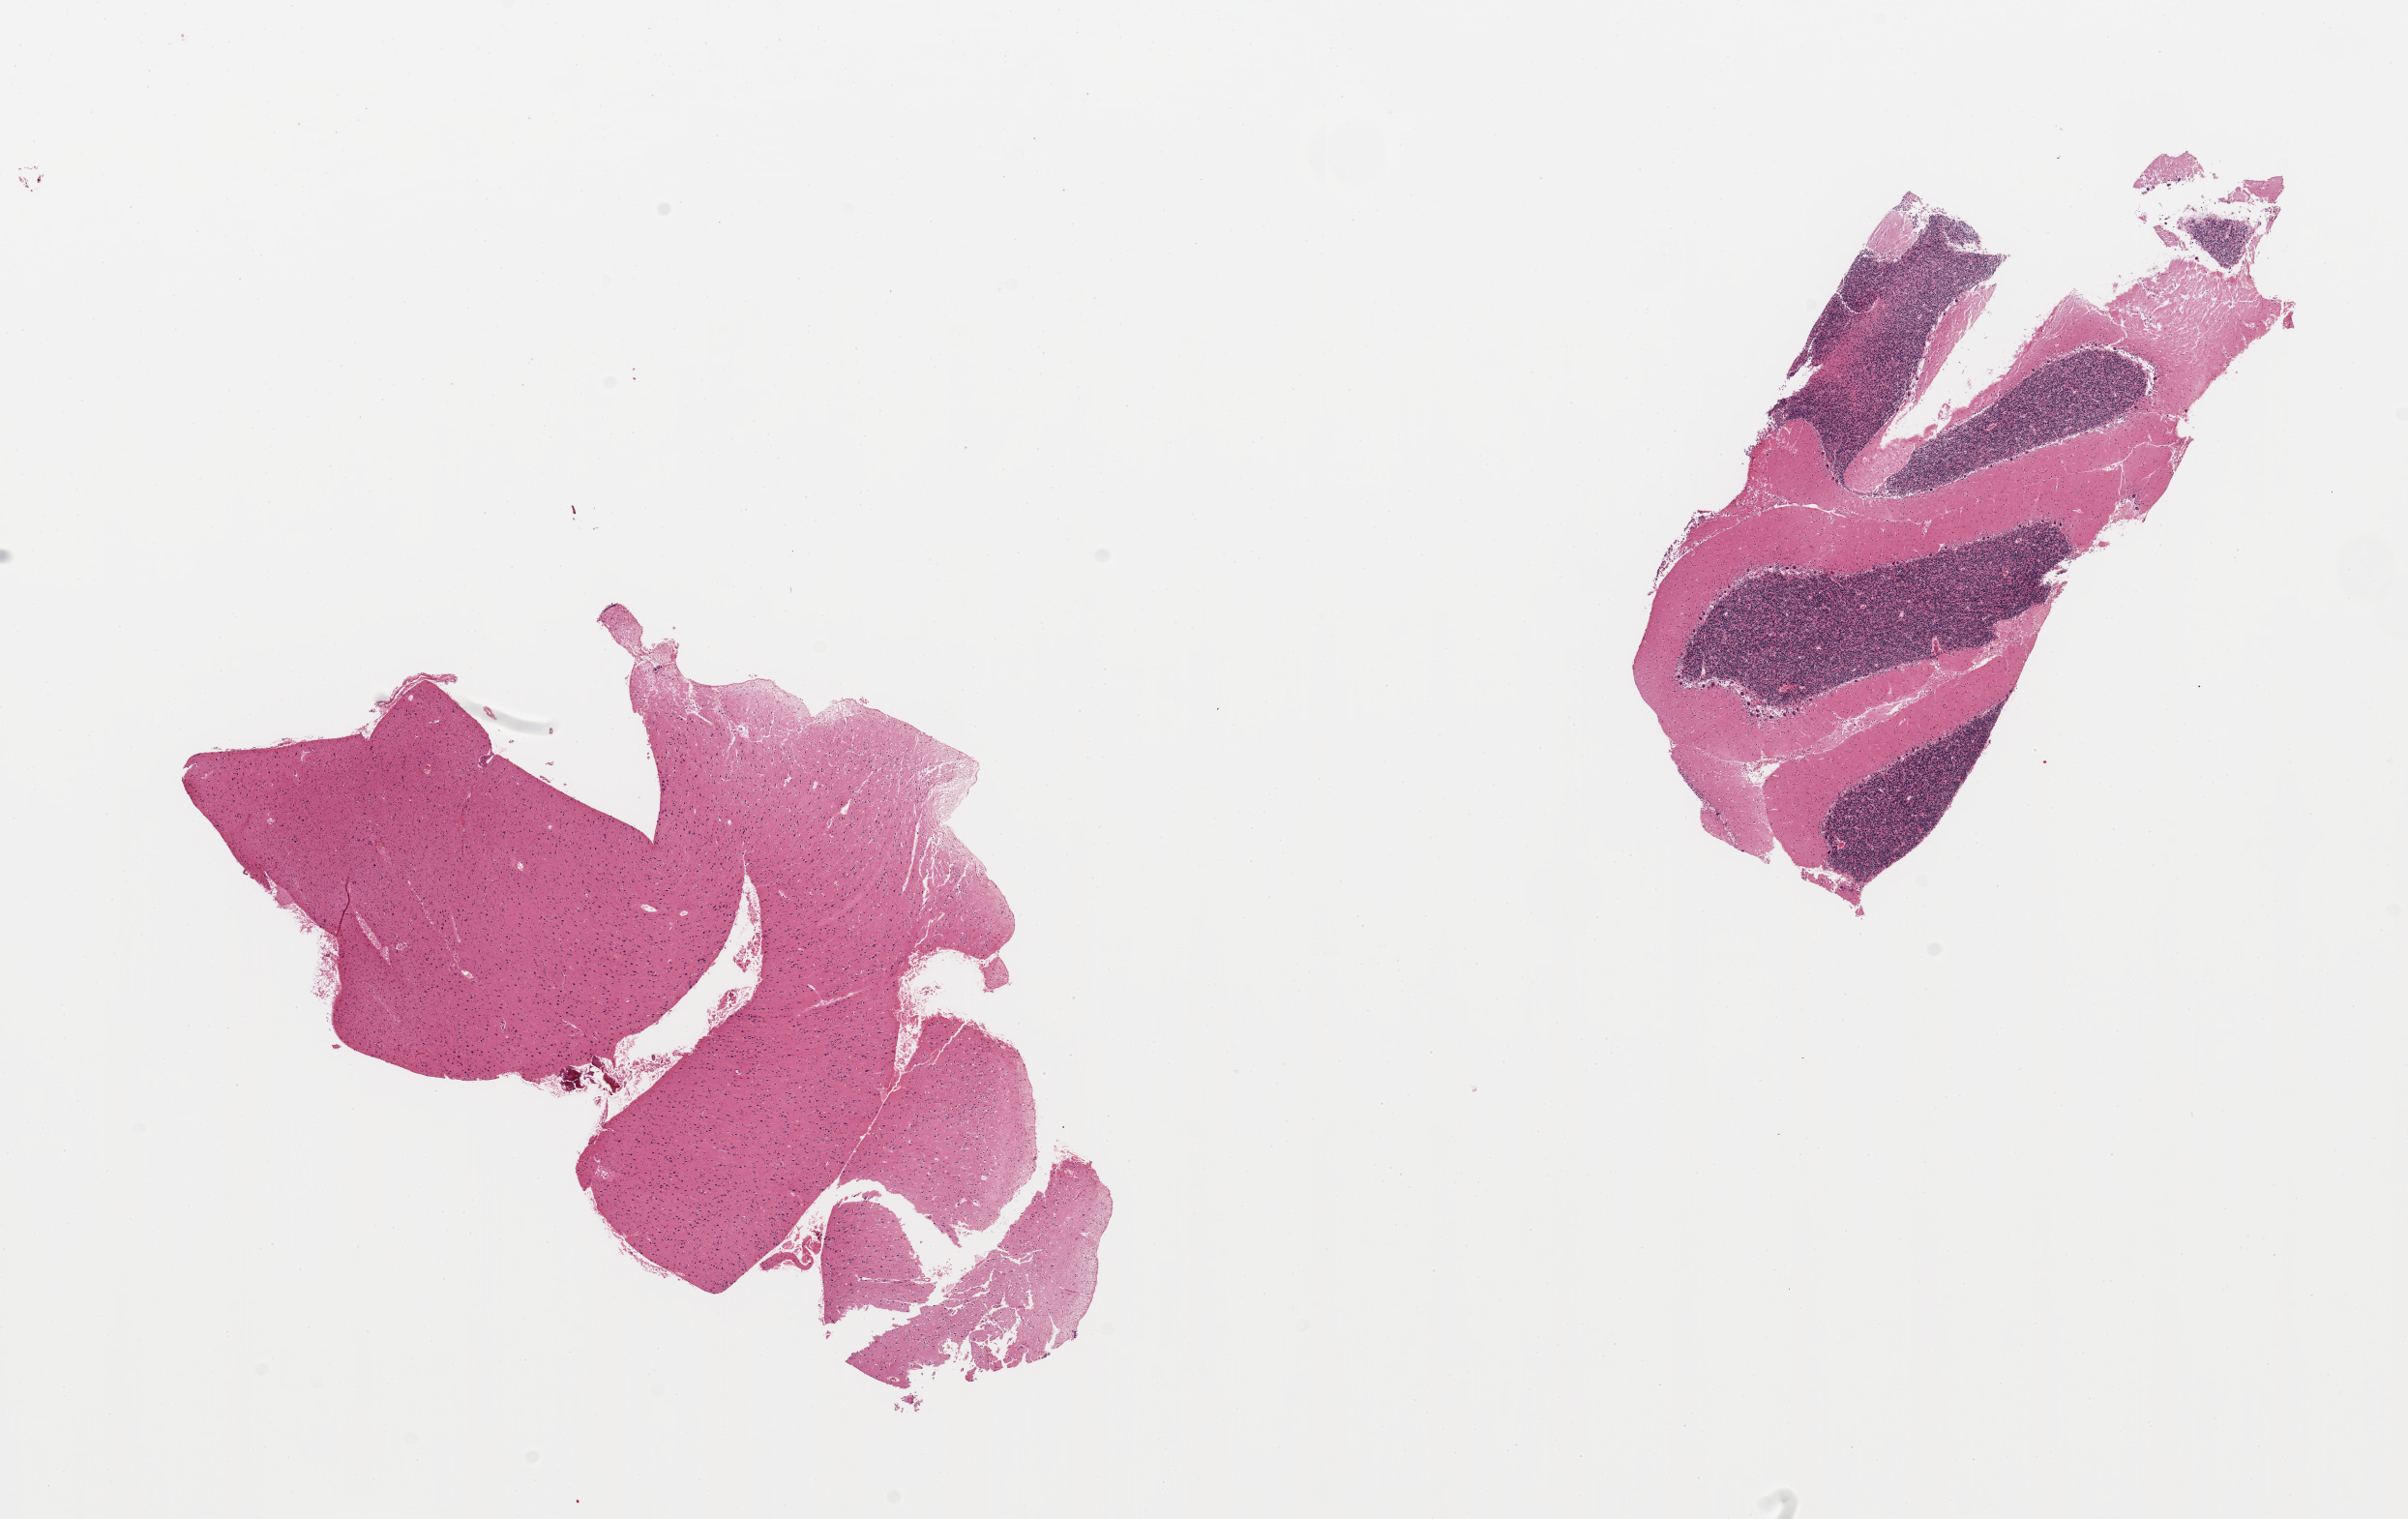
Haematoxylin and eosin whole-slide image, whole scanned area (about 19.7 x 12.4 mm, from a 20x scan) shown as a low-resolution overview, PAXgene-fixed paraffin-embedded (PFPE) section, section of cerebral cortex (target tissue), donor tissue sample. Donor: male.
Reviewer comment on this tissue sample: 2 pieces, one cortex, one cerebellum--beware upon sampling.